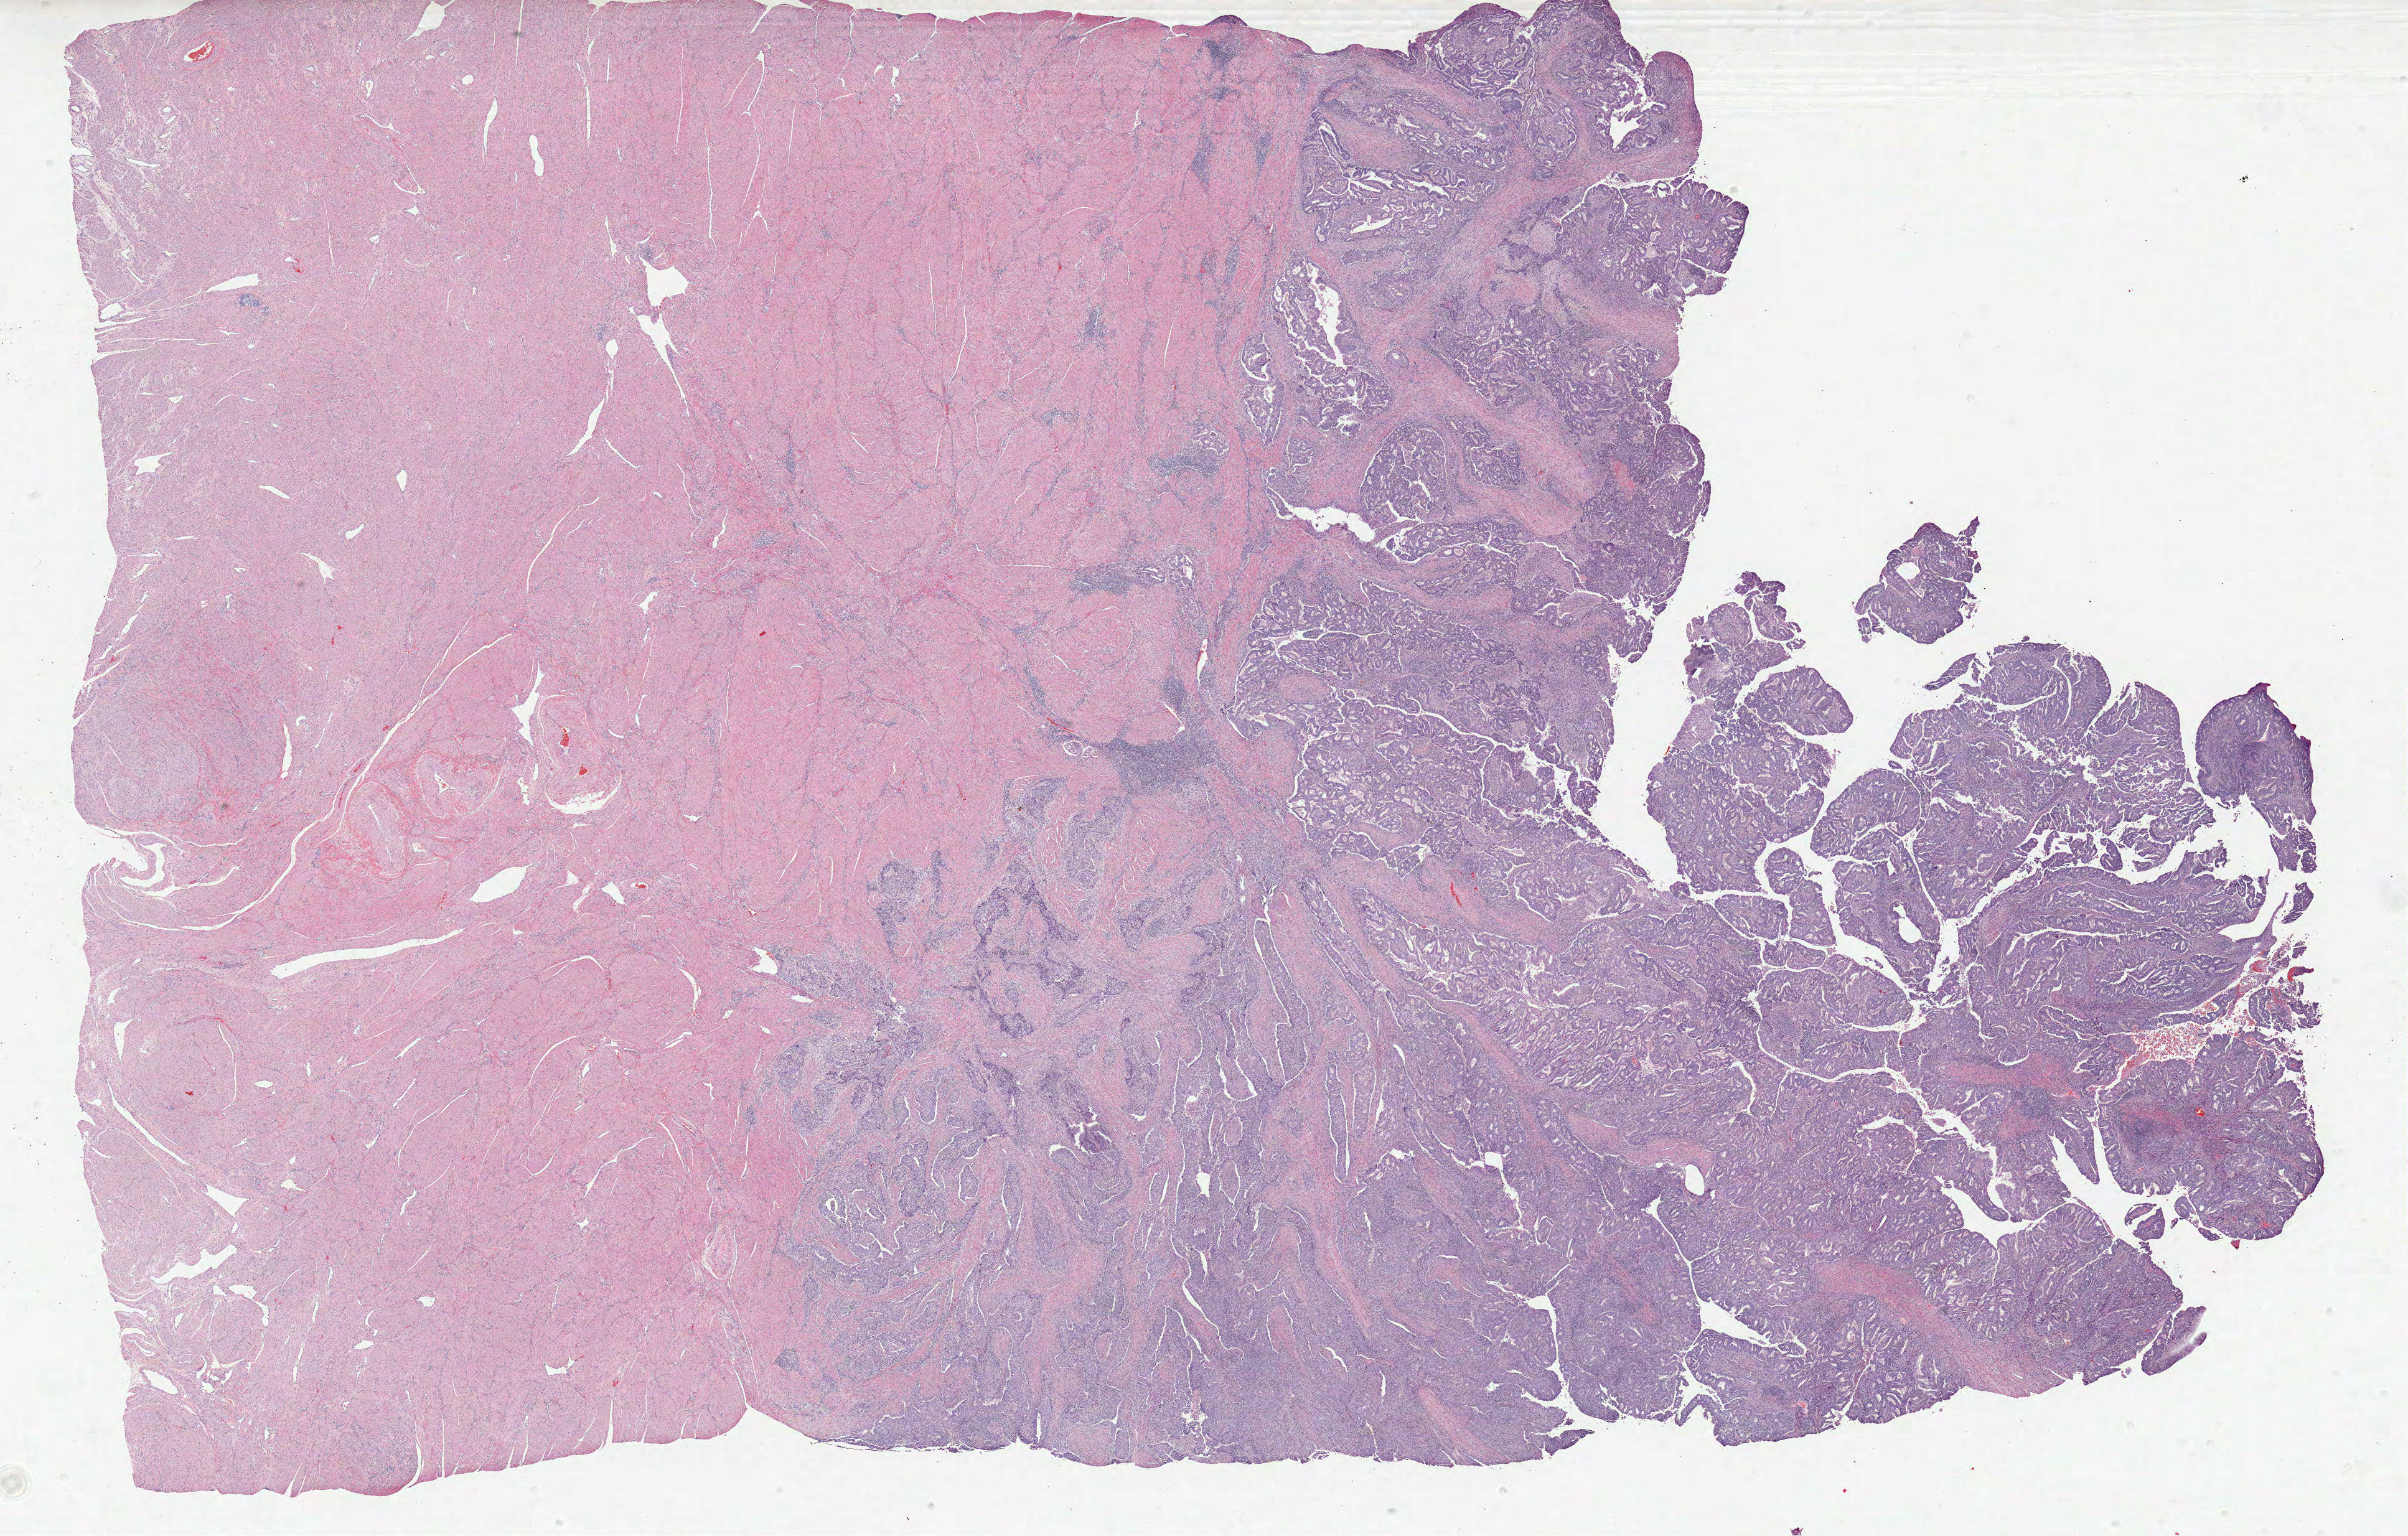
Whole-slide histology image, H&E-stained — low-resolution overview of the scanned area, about 30.8 x 19.7 mm (acquisition: 20x scan); formalin-fixed paraffin-embedded (FFPE) diagnostic section; sample: primary tumour, uterus. Female patient; age at initial diagnosis 40 years. Histologic grade: G2 (moderately differentiated).
* histologic diagnosis: Endometrioid adenocarcinoma, NOS (endometrium)
* FIGO stage: IIIC2